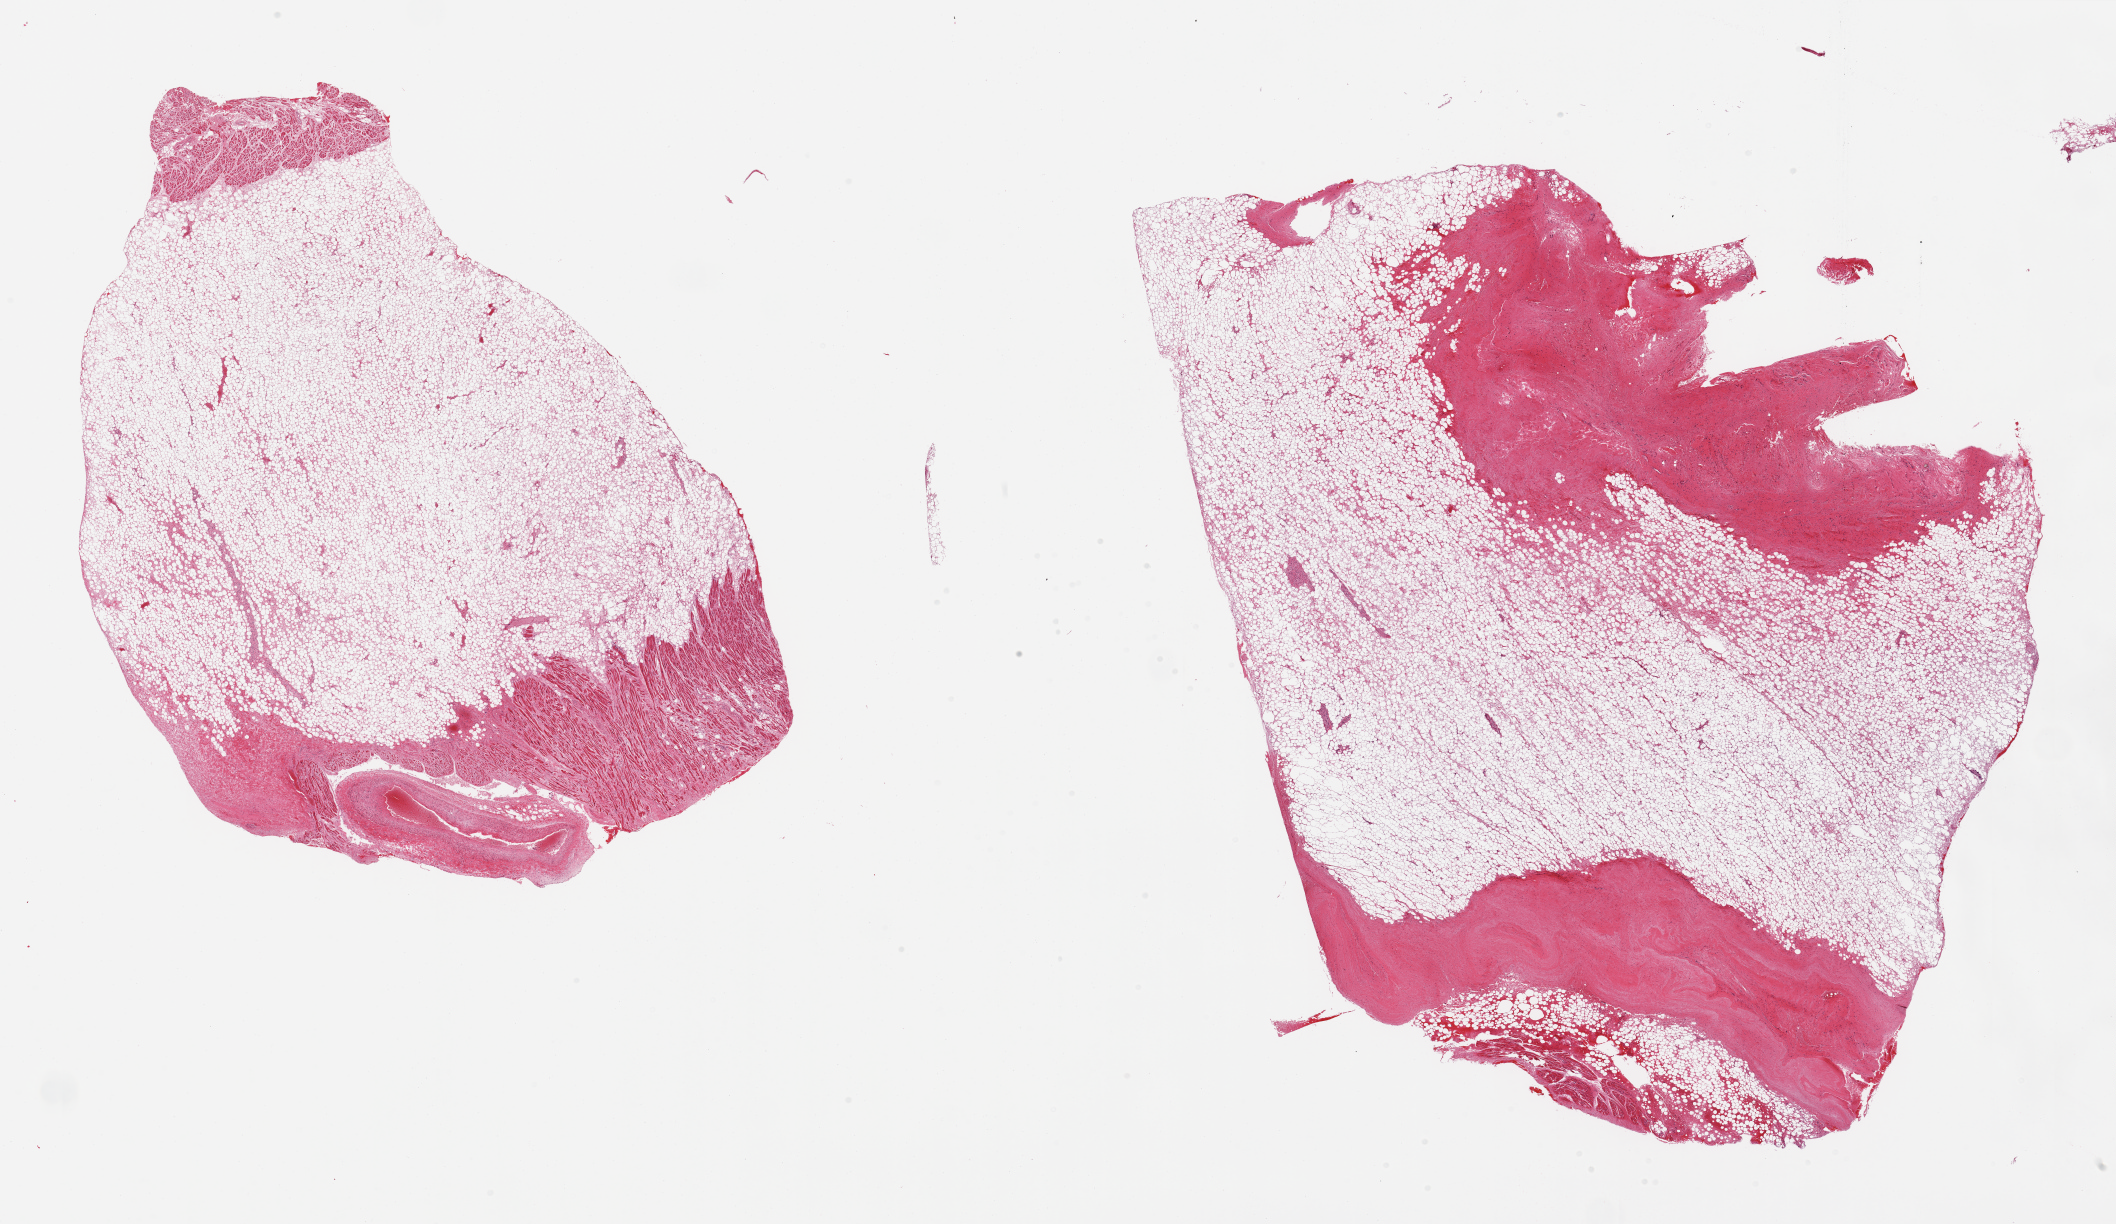
Haematoxylin and eosin whole-slide image — whole scanned area (about 33.5 x 19.4 mm, acquisition: 20x scan) shown as a low-resolution overview. PAXgene-fixed paraffin-embedded (PFPE) section. Sampled site (target tissue): auricular appendage. Tissue donor sample.
• pathologist's review note for this sample: 2 pieces, no abnormalities, ~60% interstitial/ adherent fat